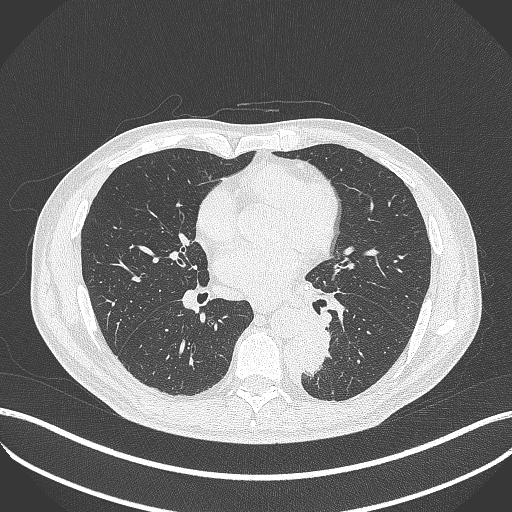
Chest CT, one axial slice; position 196 of 451 along the scan axis; lung window (W 1500 / L -600 HU); 1 mm slice thickness; 512 × 512 image matrix. Patient: male, 72 years. From the clinical record (not read from this slice): clinical TNM (as recorded): T2b N0 M1.
Structures marked on this image (bounding box drawn by a radiologist):
- lung tumour (recorded histology: adenocarcinoma): bounding box (x1, y1, x2, y2) in pixels: (301, 320, 332, 381)